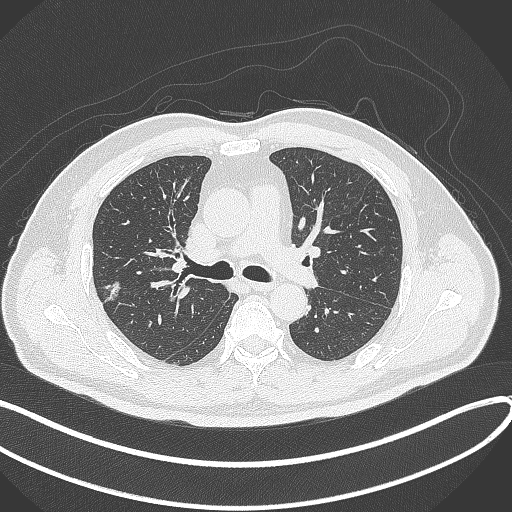
Chest CT, one axial slice; slice 212 of 372 in the series (ordered by position); lung window (W 1500 / L -600 HU); 512 × 512 image matrix. Patient: male, 60 years. From the clinical record (not read from this slice): clinical TNM (as recorded): T1c N0 M0.
Structures marked on this image (bounding box drawn by a radiologist):
- lung tumour (recorded histology: adenocarcinoma): box from (x=96, y=278) to (x=126, y=310) px